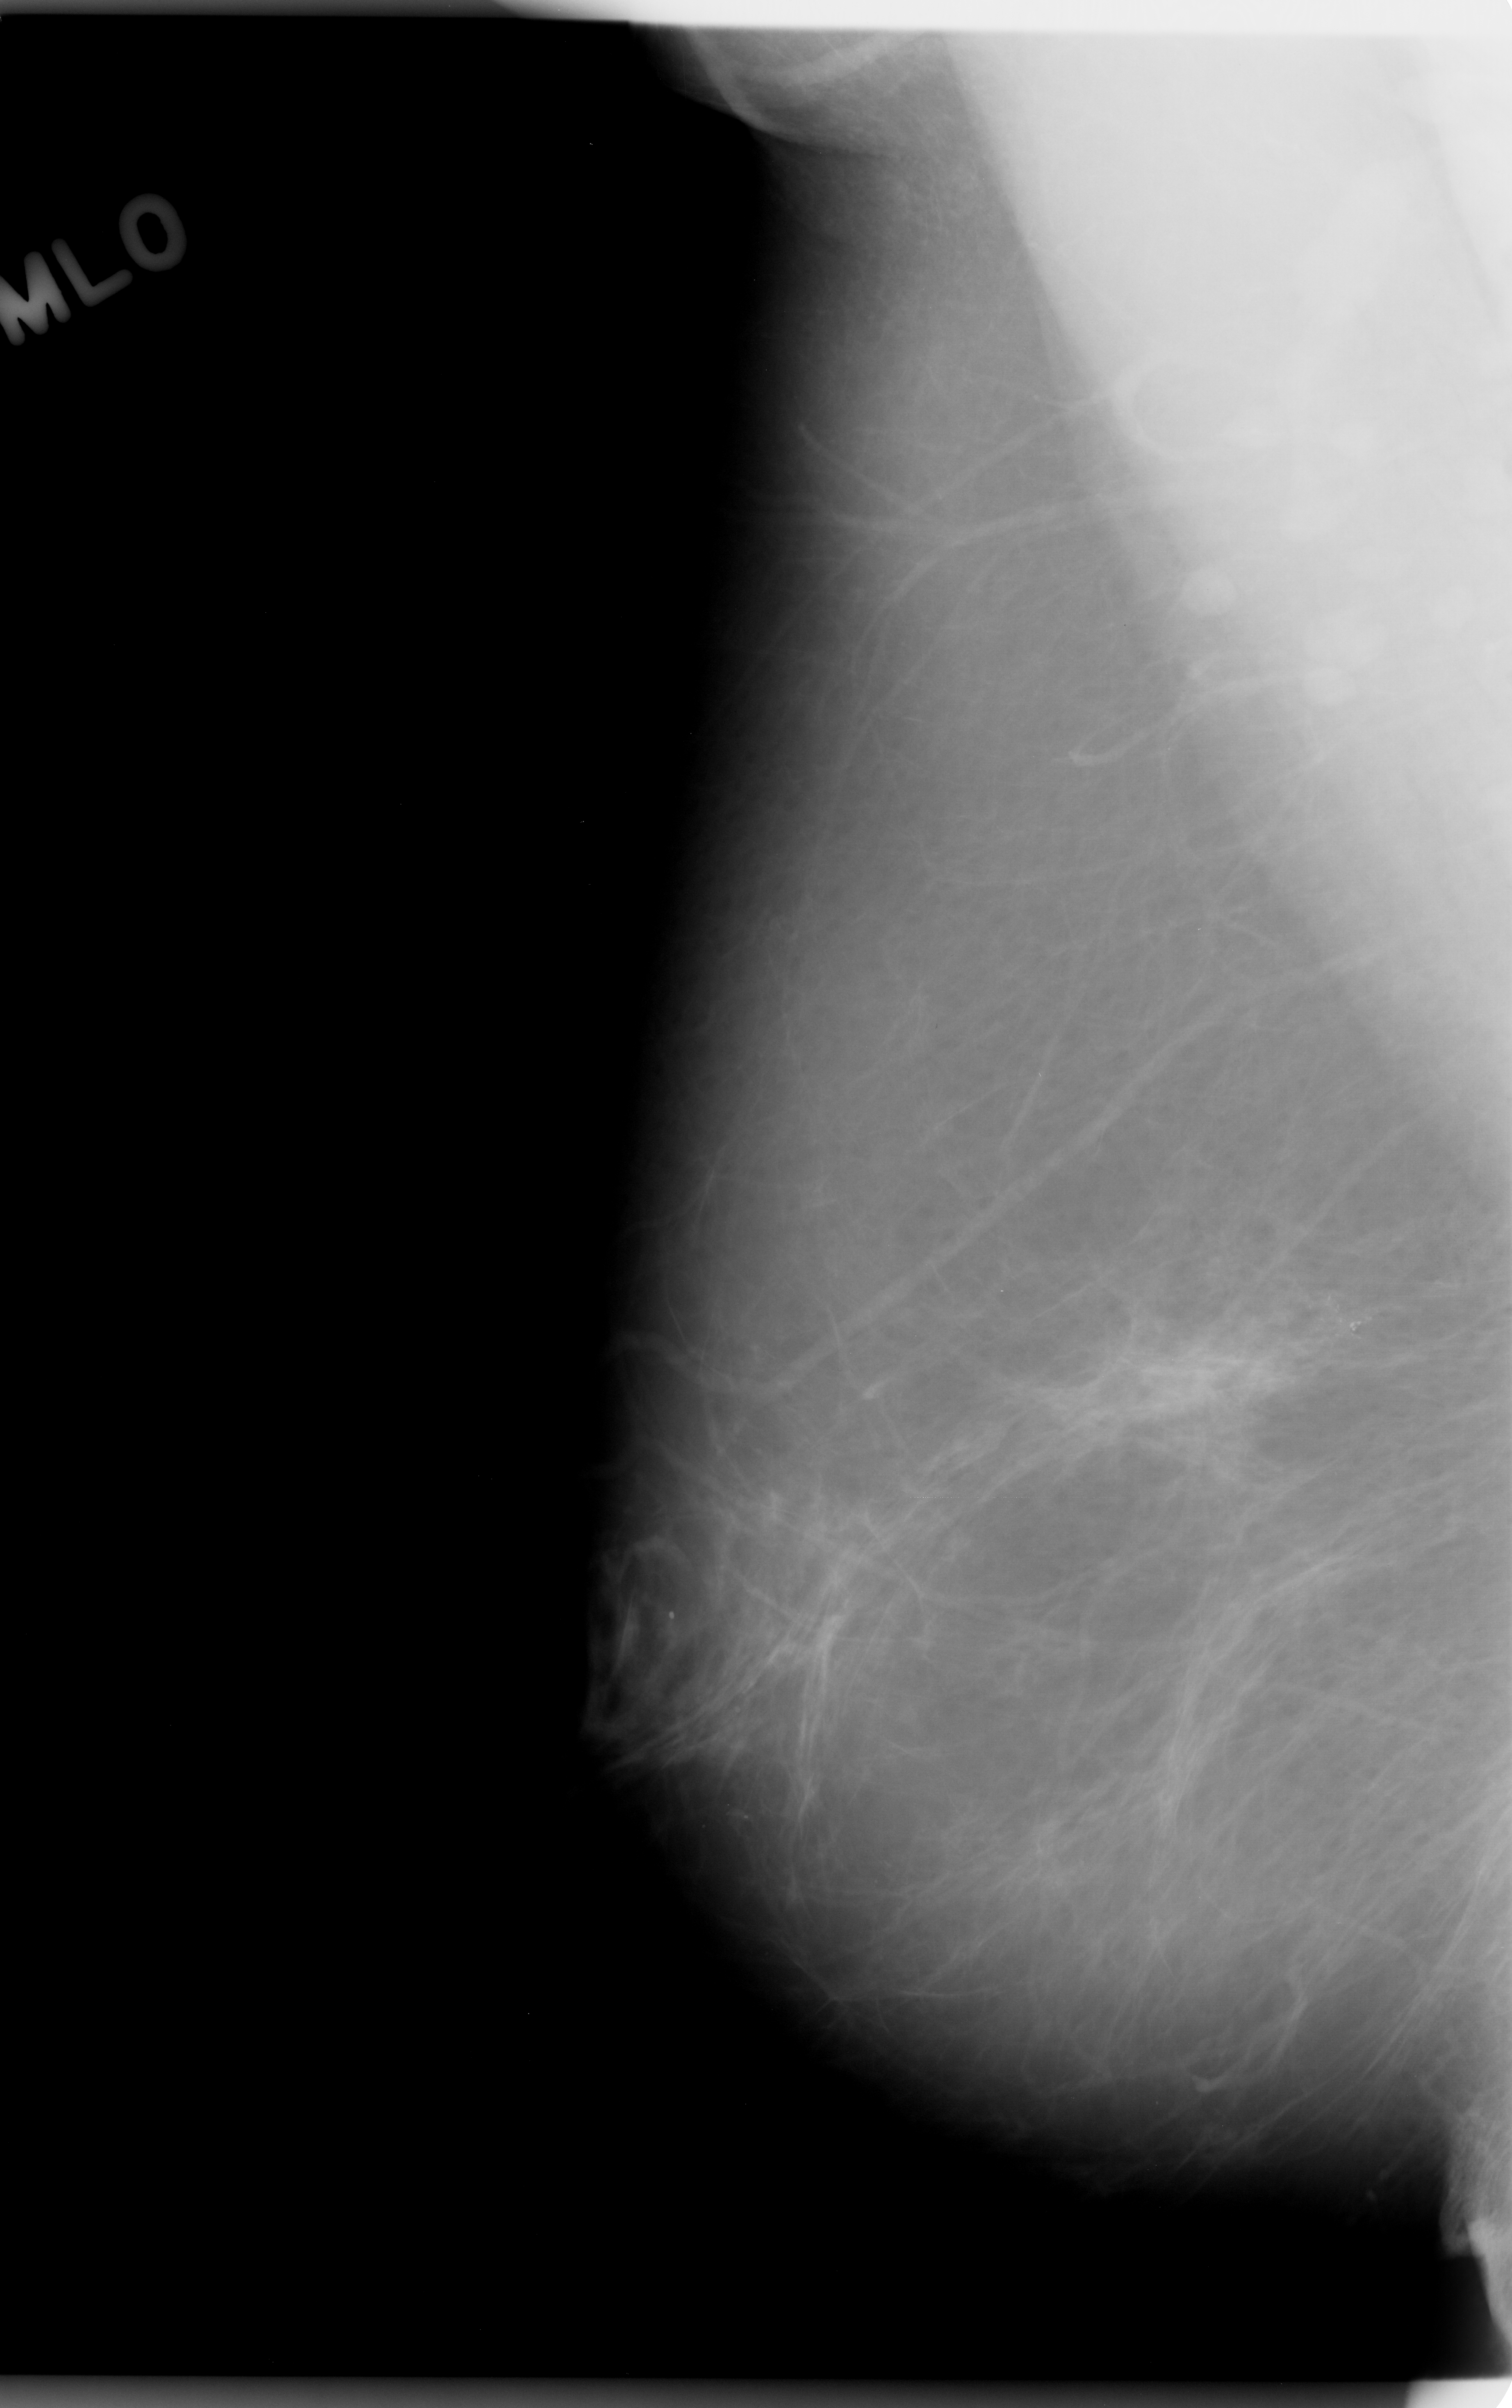
Mammogram (digitized film); right breast; mediolateral oblique (MLO) view; BI-RADS breast density category 1 (scale 1–4).
Marked abnormality: calcifications, morphology amorphous, distribution clustered; BI-RADS assessment category 4; pathology result (as recorded, not read from the image): malignant.